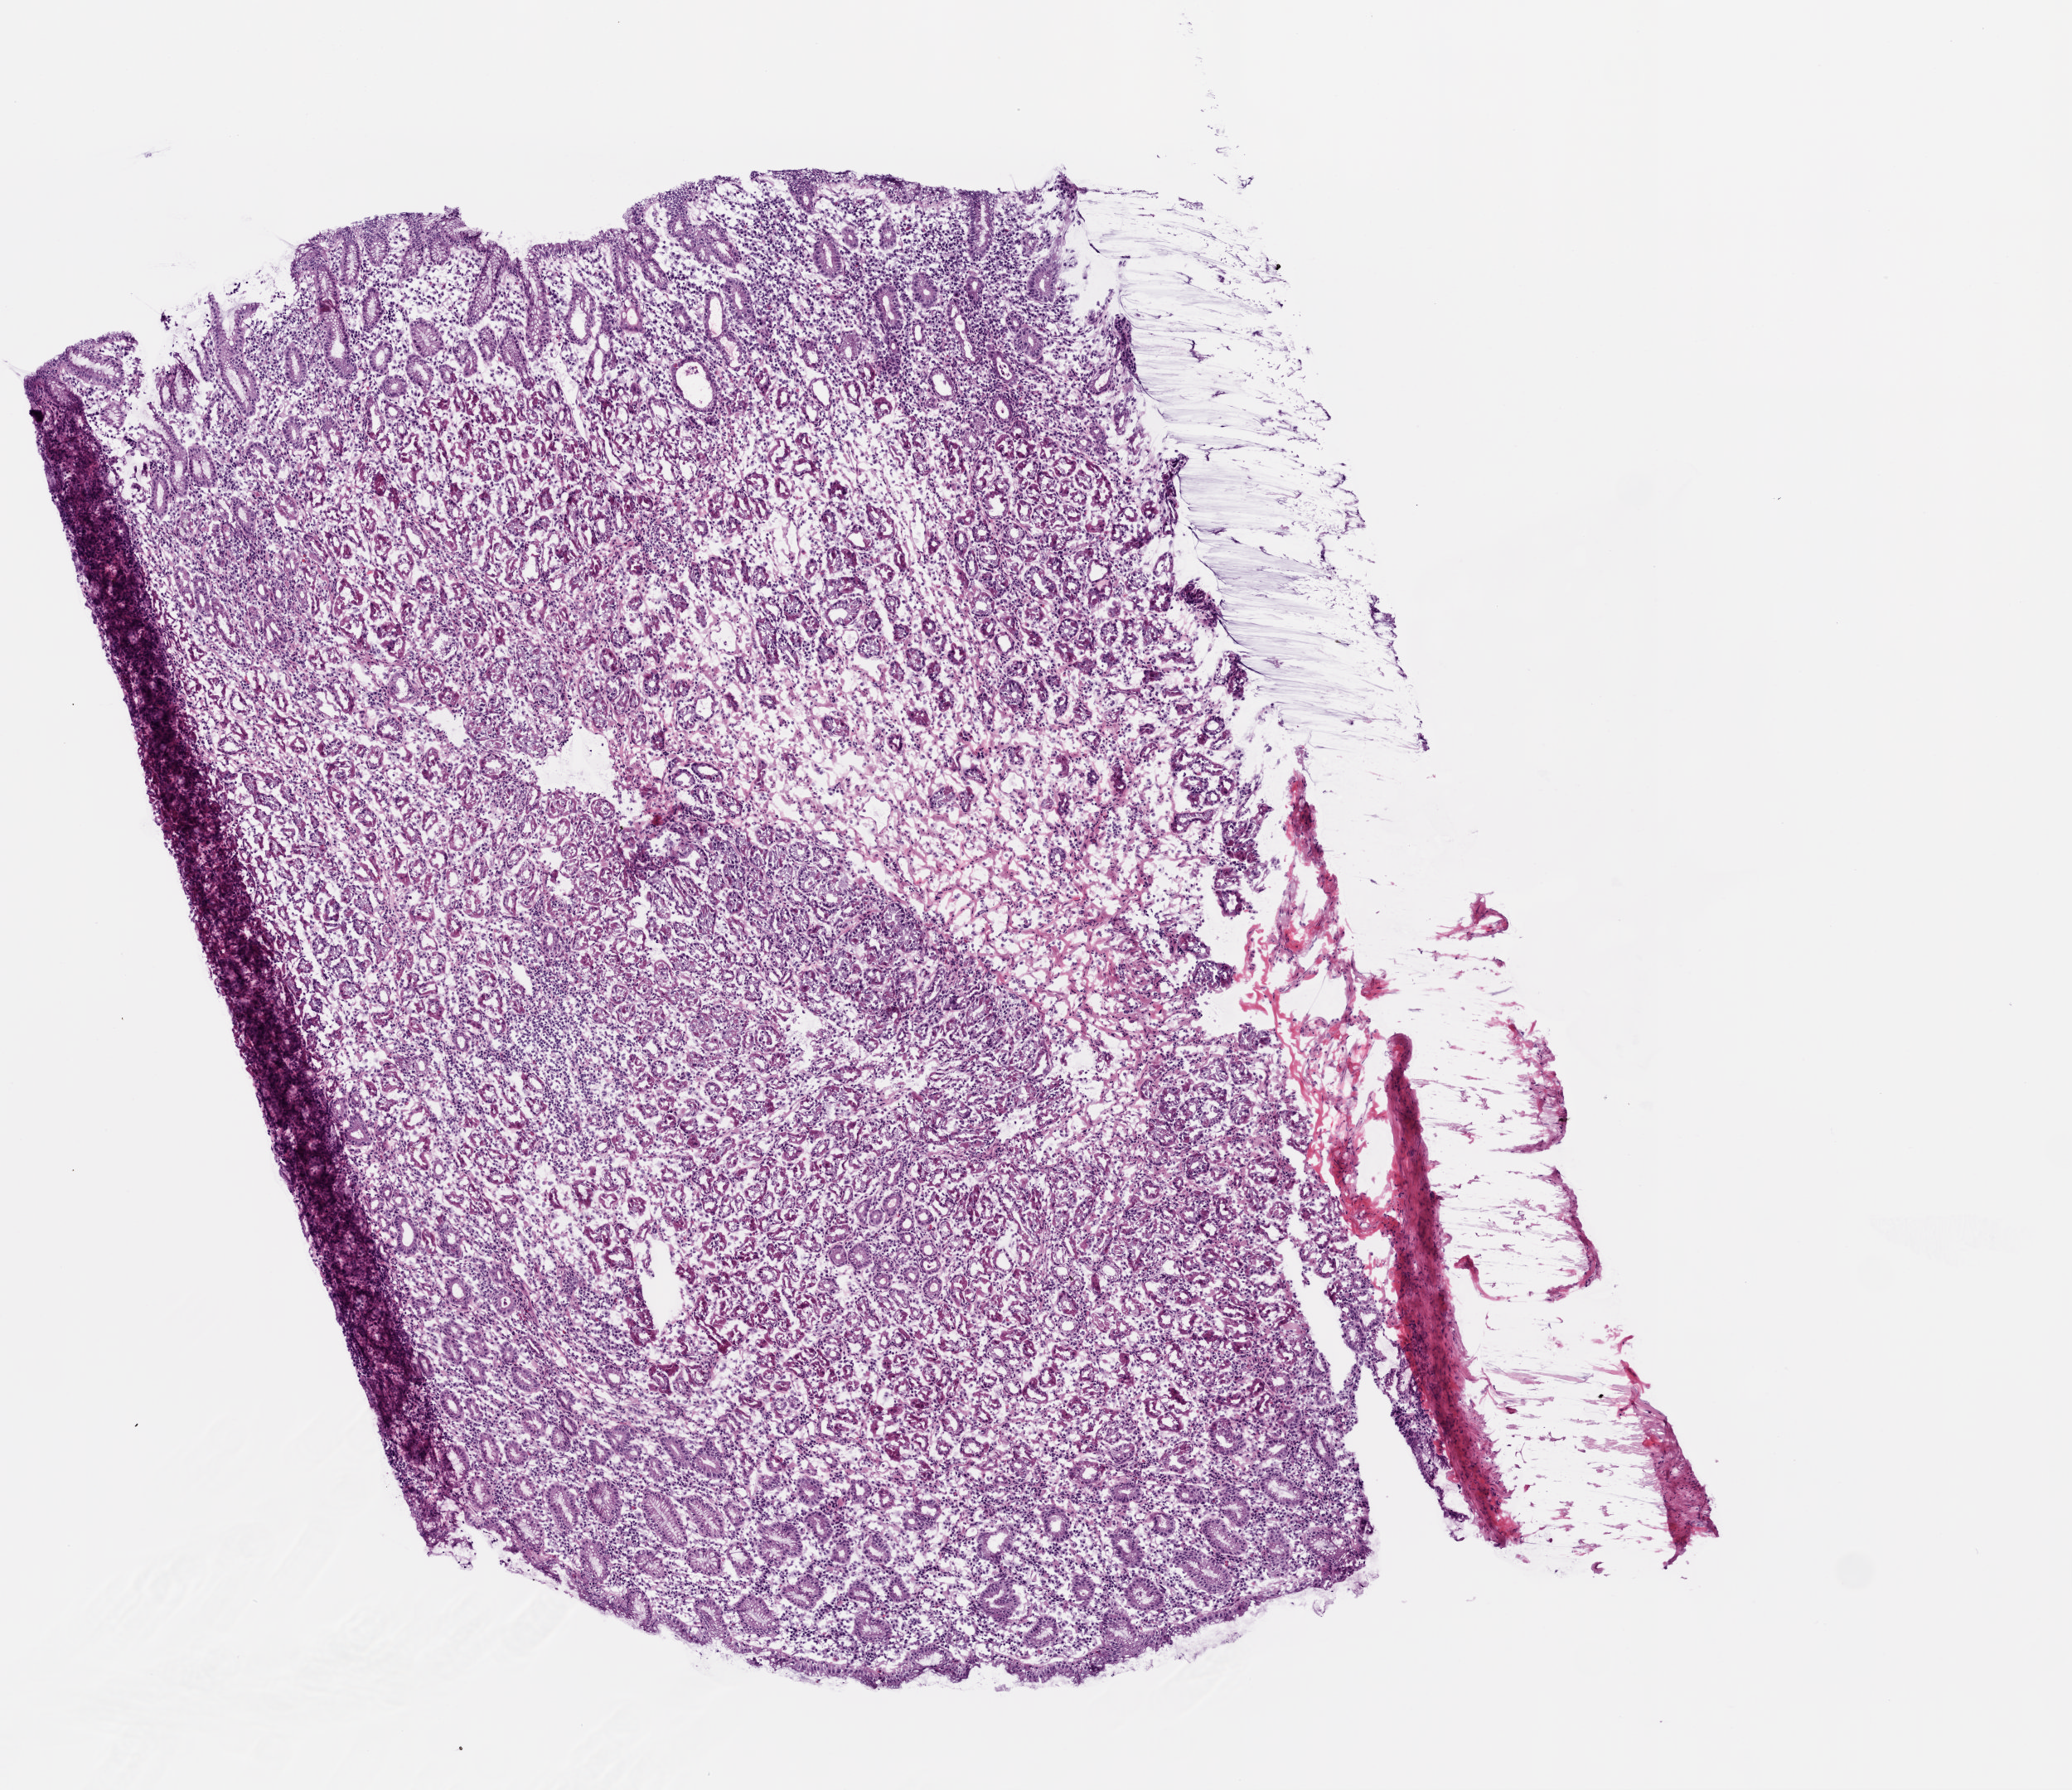
H&E whole-slide image, shown as a low-resolution overview of the whole scanned area (about 5.0 x 4.3 mm); frozen section from the top of the tissue portion; solid tissue normal (non-tumour tissue) sample from the stomach. Male, age 58 years at initial diagnosis.
This section: solid tissue normal sample (biorepository sample class). Patient diagnosis: Adenocarcinoma, intestinal type.